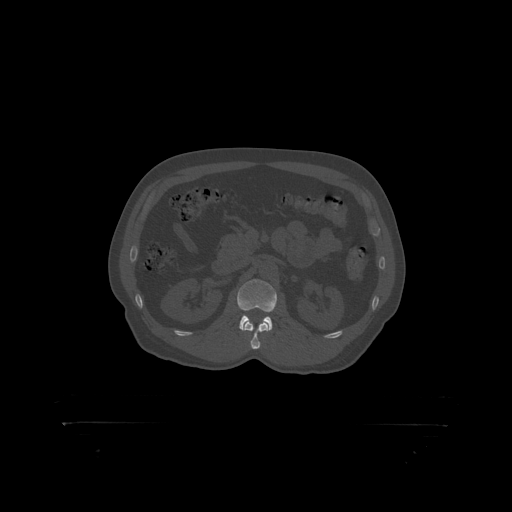
CT including the spine, one axial slice; slice 309 of 399 in the series (ordered by position); 120 kVp; bone window (W 1800 / L 400 HU); 1.25 mm slice thickness; 512 × 512 image matrix, field of view 650 × 650 mm. Male patient, age 46 years. From the clinical record (not read from this slice): primary cancer: skin.
Annotated regions visible in this slice (semi-automatically segmented with operator editing):
- L2 vertebra: bounding box <238,280,277,319> (left, top, right, bottom; pixels)